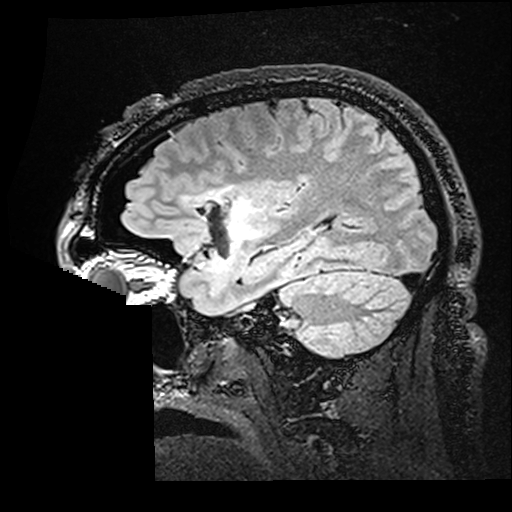
Brain MRI from a brain-tumour surgery series, one sagittal slice; slice 120 of 176 in the series (ordered by position); T2 FLAIR; 512 × 512 image matrix, field of view 250 × 250 mm. From the clinical record (not read from this slice): histopathology: Astrocytoma; WHO grade: 2; IDH mutation: yes.
Annotated regions visible in this slice (expert manual segmentation):
- residual tumour: bounding box (x1, y1, x2, y2) in pixels: (183, 186, 265, 243)